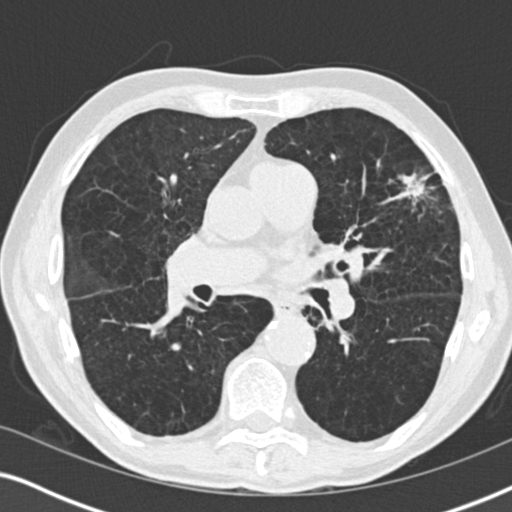
Low-dose screening chest CT, one axial slice; position 104 of 196 along the scan axis; lung window (W 1500 / L -600 HU); 2 mm slice thickness; 512 × 512 image matrix, field of view 330 × 330 mm.
Annotated regions visible in this slice (outlined manually by an expert reader):
- lesion 1 (tumor, upper lobe of left lung): box from (x=397, y=175) to (x=427, y=200) px